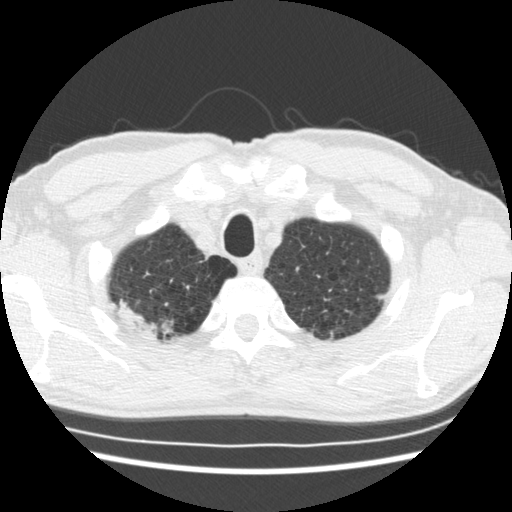
Low-dose screening chest CT, one axial slice. Position 160 of 183 along the scan axis. Reconstruction kernel STANDARD. Lung window (W 1500 / L -600 HU). 2.5 mm slice thickness. 512 × 512 image matrix, field of view 339 × 339 mm.
Annotated regions visible in this slice (expert manual segmentation):
- lesion 1 (tumor, upper lobe of right lung): bounding box <117,306,157,340> (left, top, right, bottom; pixels)